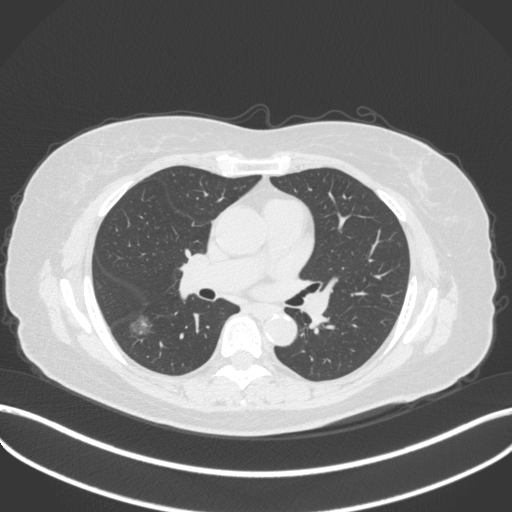
Chest CT, one axial slice. Slice 175 of 322 in the series (ordered by position). Reconstruction kernel B31f. Lung window (W 1500 / L -600 HU). 1 mm slice thickness. 512 × 512 image matrix, field of view 400 × 400 mm. Female patient, age 64 years. Case-level facts recorded for this patient, not image findings: clinical TNM (as recorded): T1c N0 M0; histopathological grade: G1.
Outlined on this slice (bounding box drawn by a radiologist):
- lung tumour (recorded histology: adenocarcinoma): bounding box [x1, y1, x2, y2] px = [130, 312, 155, 339]